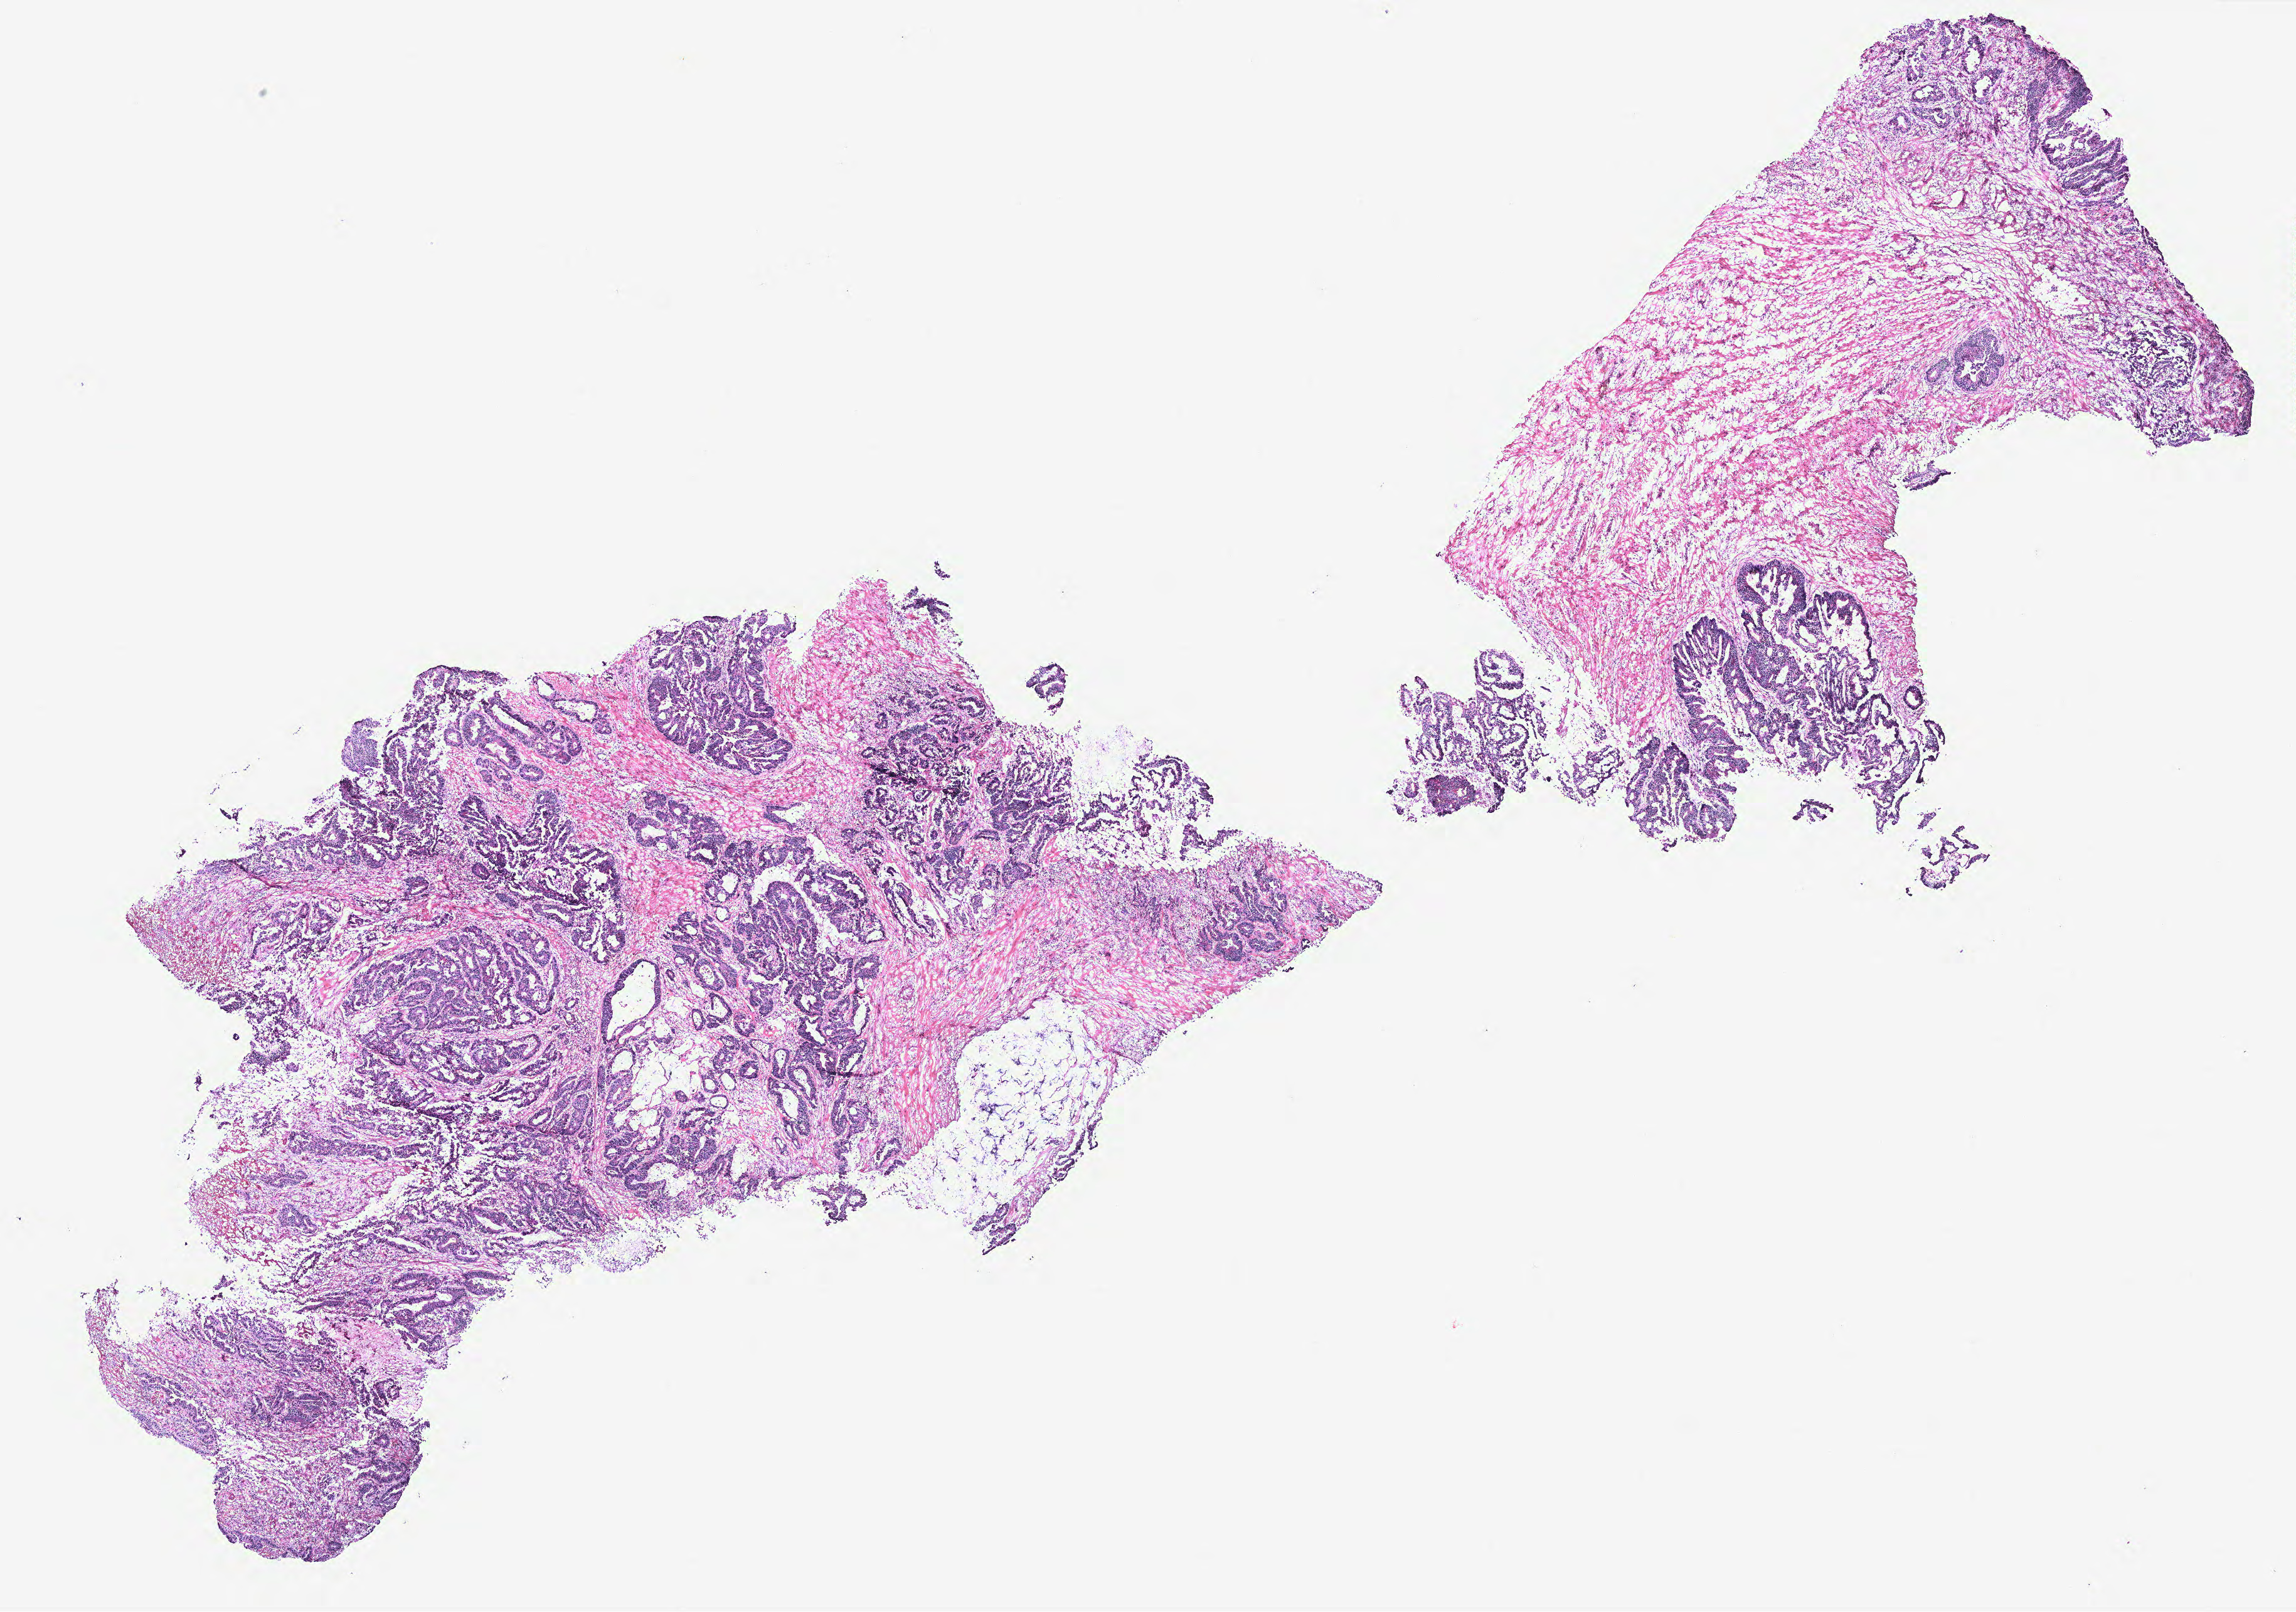
Whole-slide histology image, H&E — low-resolution overview of the scanned area, about 14.6 x 10.3 mm (slide scanned at 40x); colon, tissue type not recorded.
* patient diagnosis (cohort enrolment): colon cancer (colon)